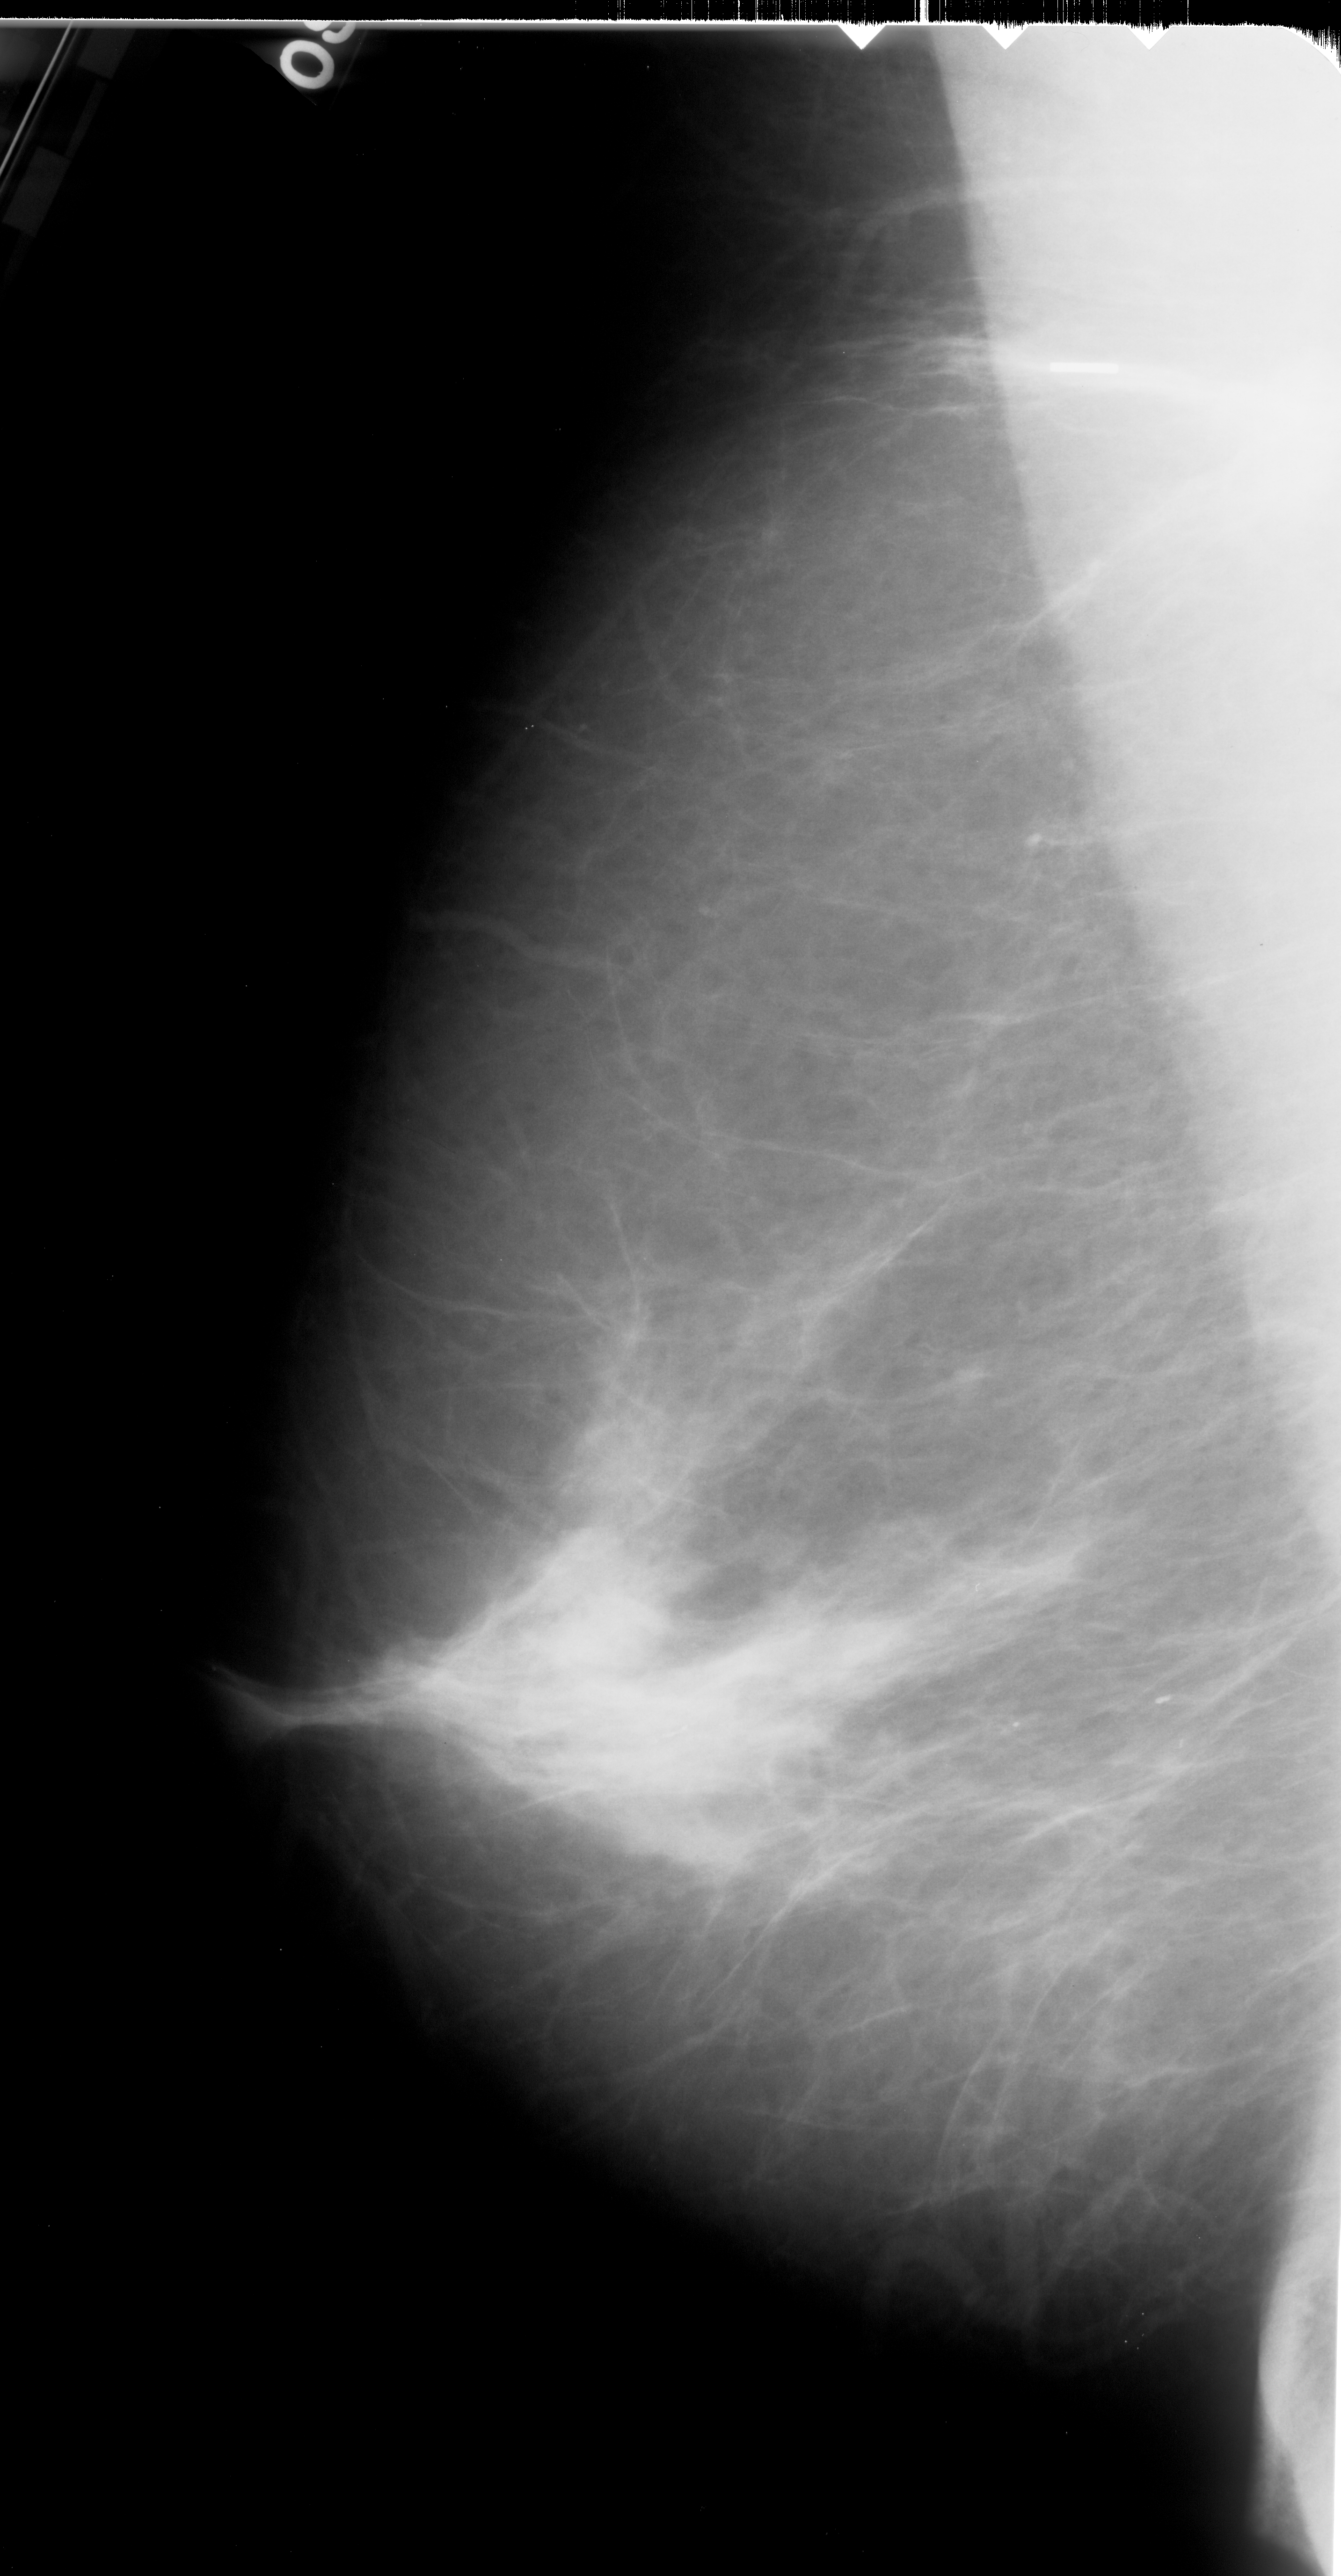
Digitized screen-film mammogram. Left breast. Mediolateral oblique (MLO) view. BI-RADS breast density category 2 (scale 1–4). 1341 × 2576 image matrix.
Expert-marked regions of interest on this image (one box per marked abnormality):
- calcifications, morphology fine linear branching, distribution linear; BI-RADS assessment category 4; pathology (as recorded): malignant: bounding box <623,1706,708,1763> (left, top, right, bottom; pixels)